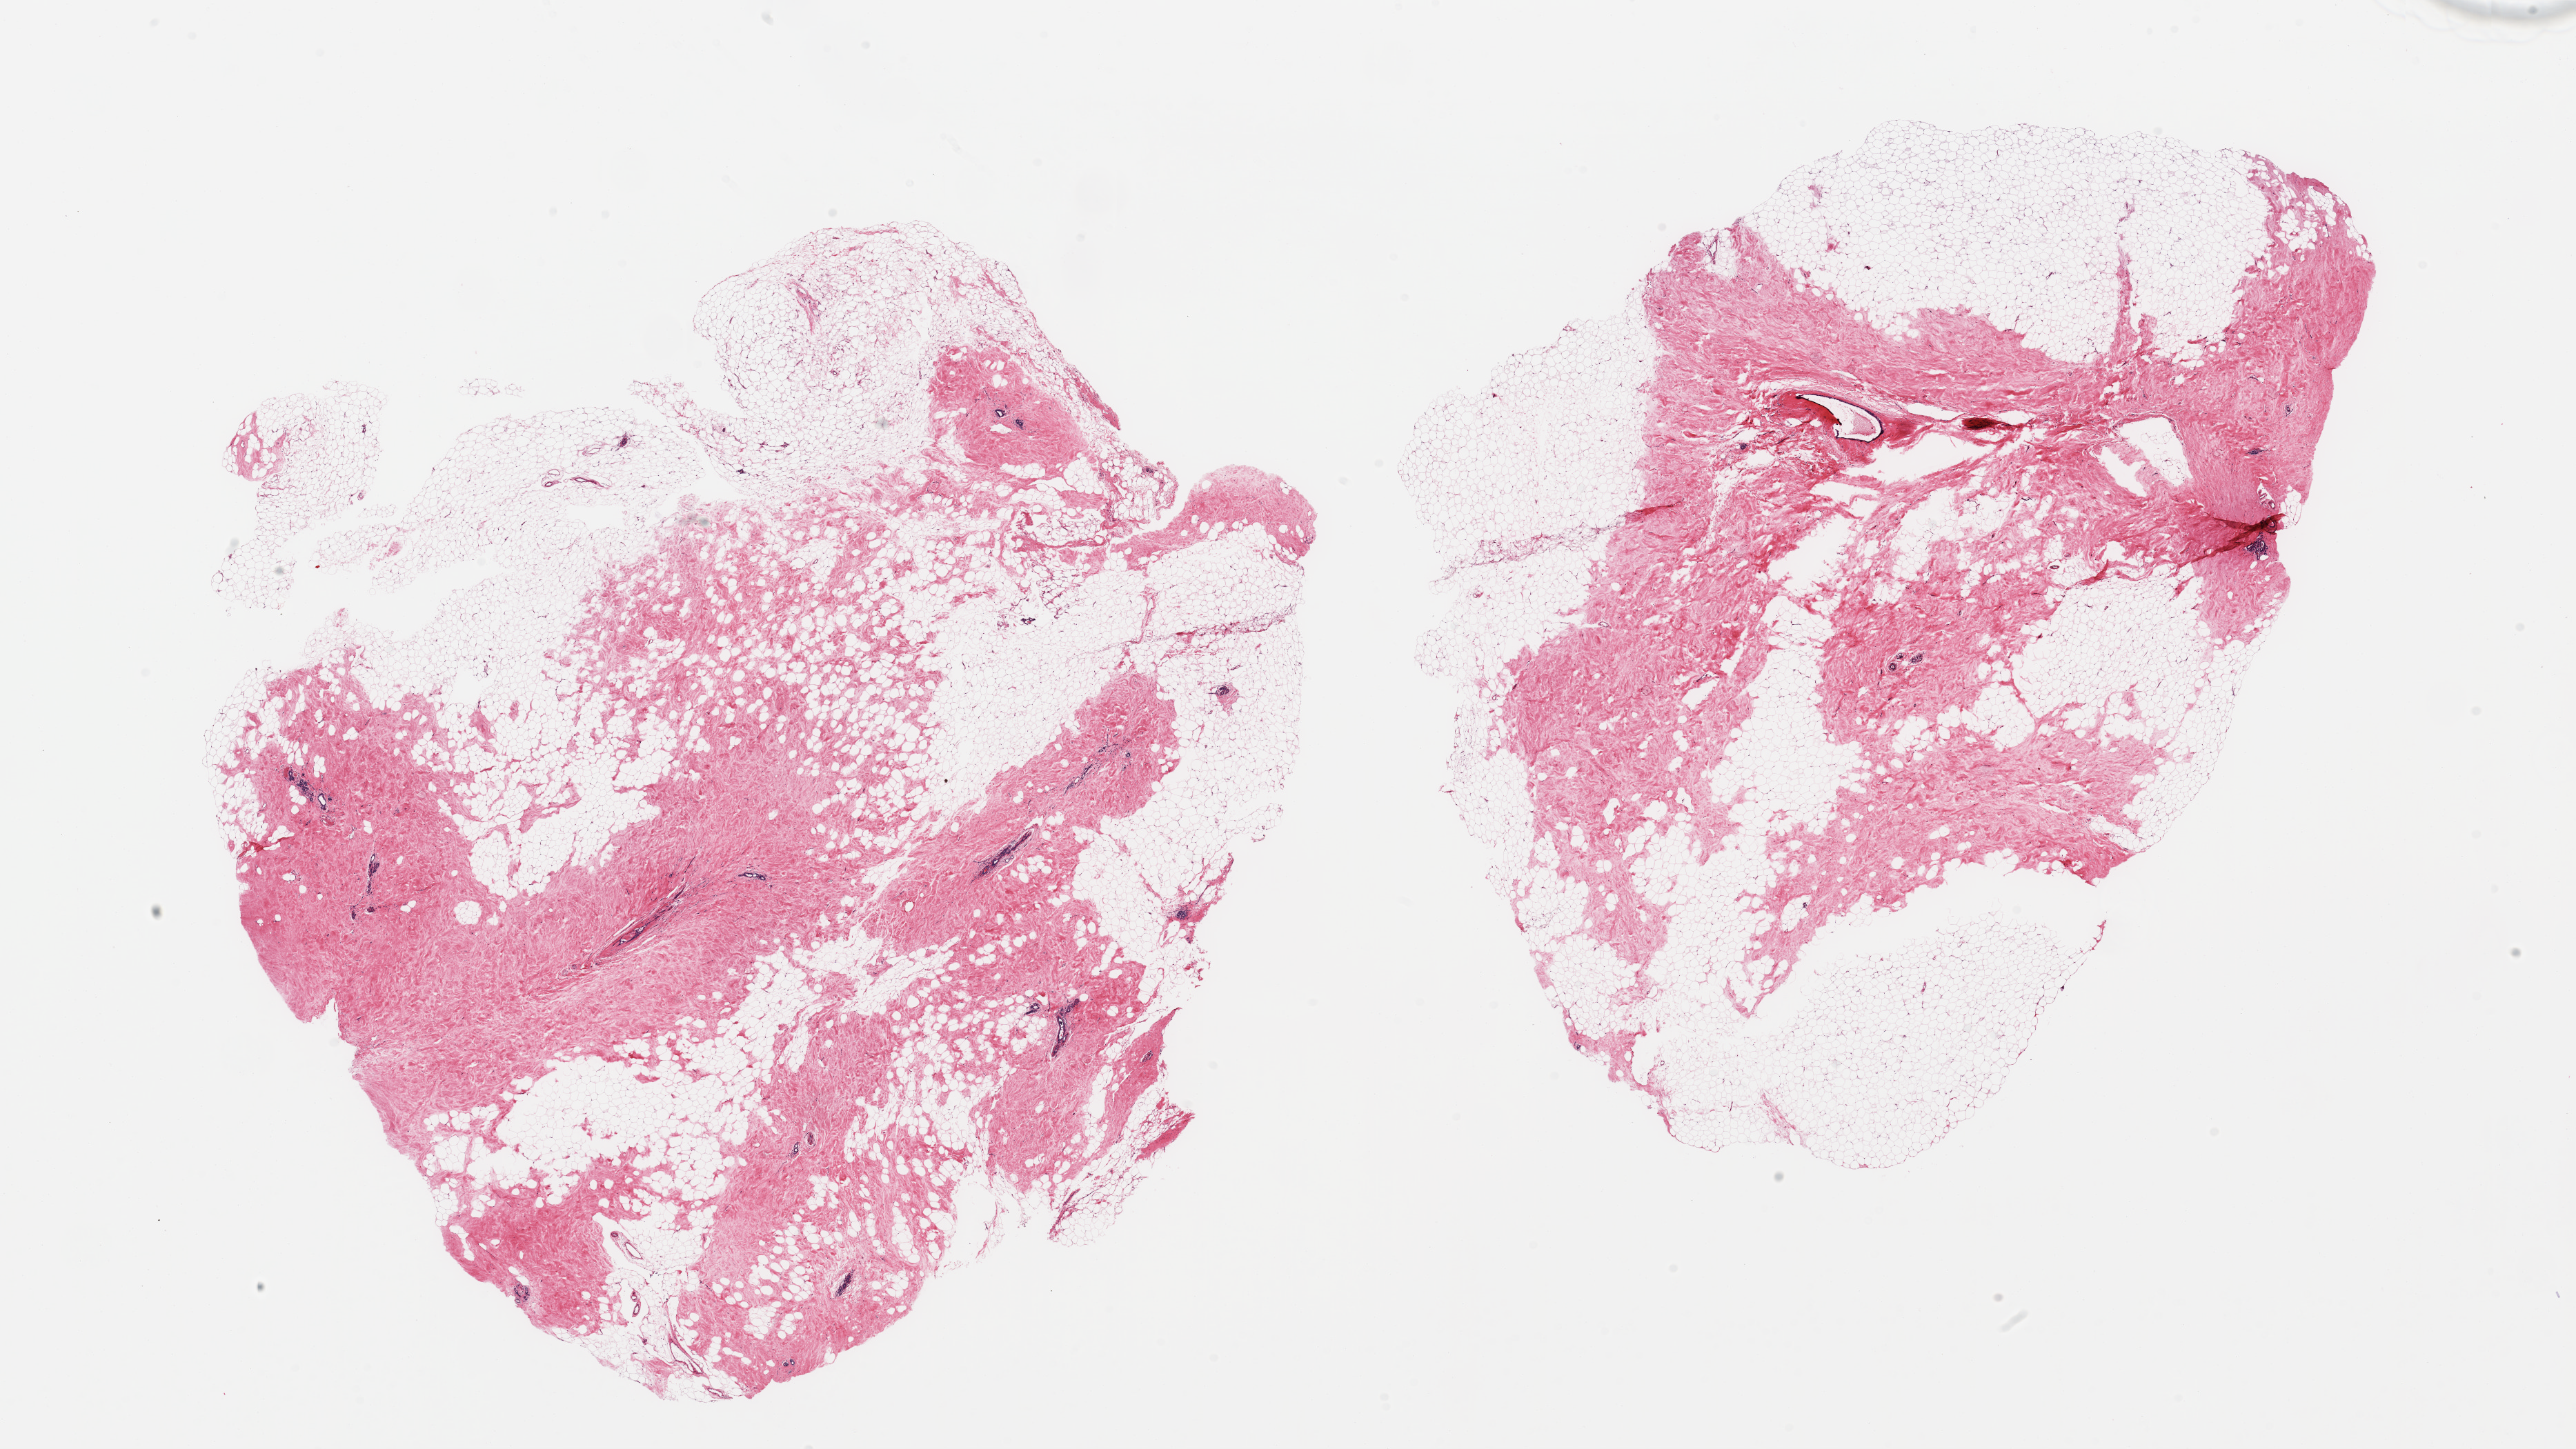
Hematoxylin and eosin (H&E) whole-slide image, brightfield — a low-resolution overview of the entire scanned area, about 29.5 x 16.6 mm; PAXgene-fixed paraffin-embedded (PFPE) section; sampled site (target tissue): breast; donor tissue sample. Donor sex: female.
Reviewer comment on this tissue sample: 2 pieces; atrophic ducts and lobular units in fibrofatty stroma.